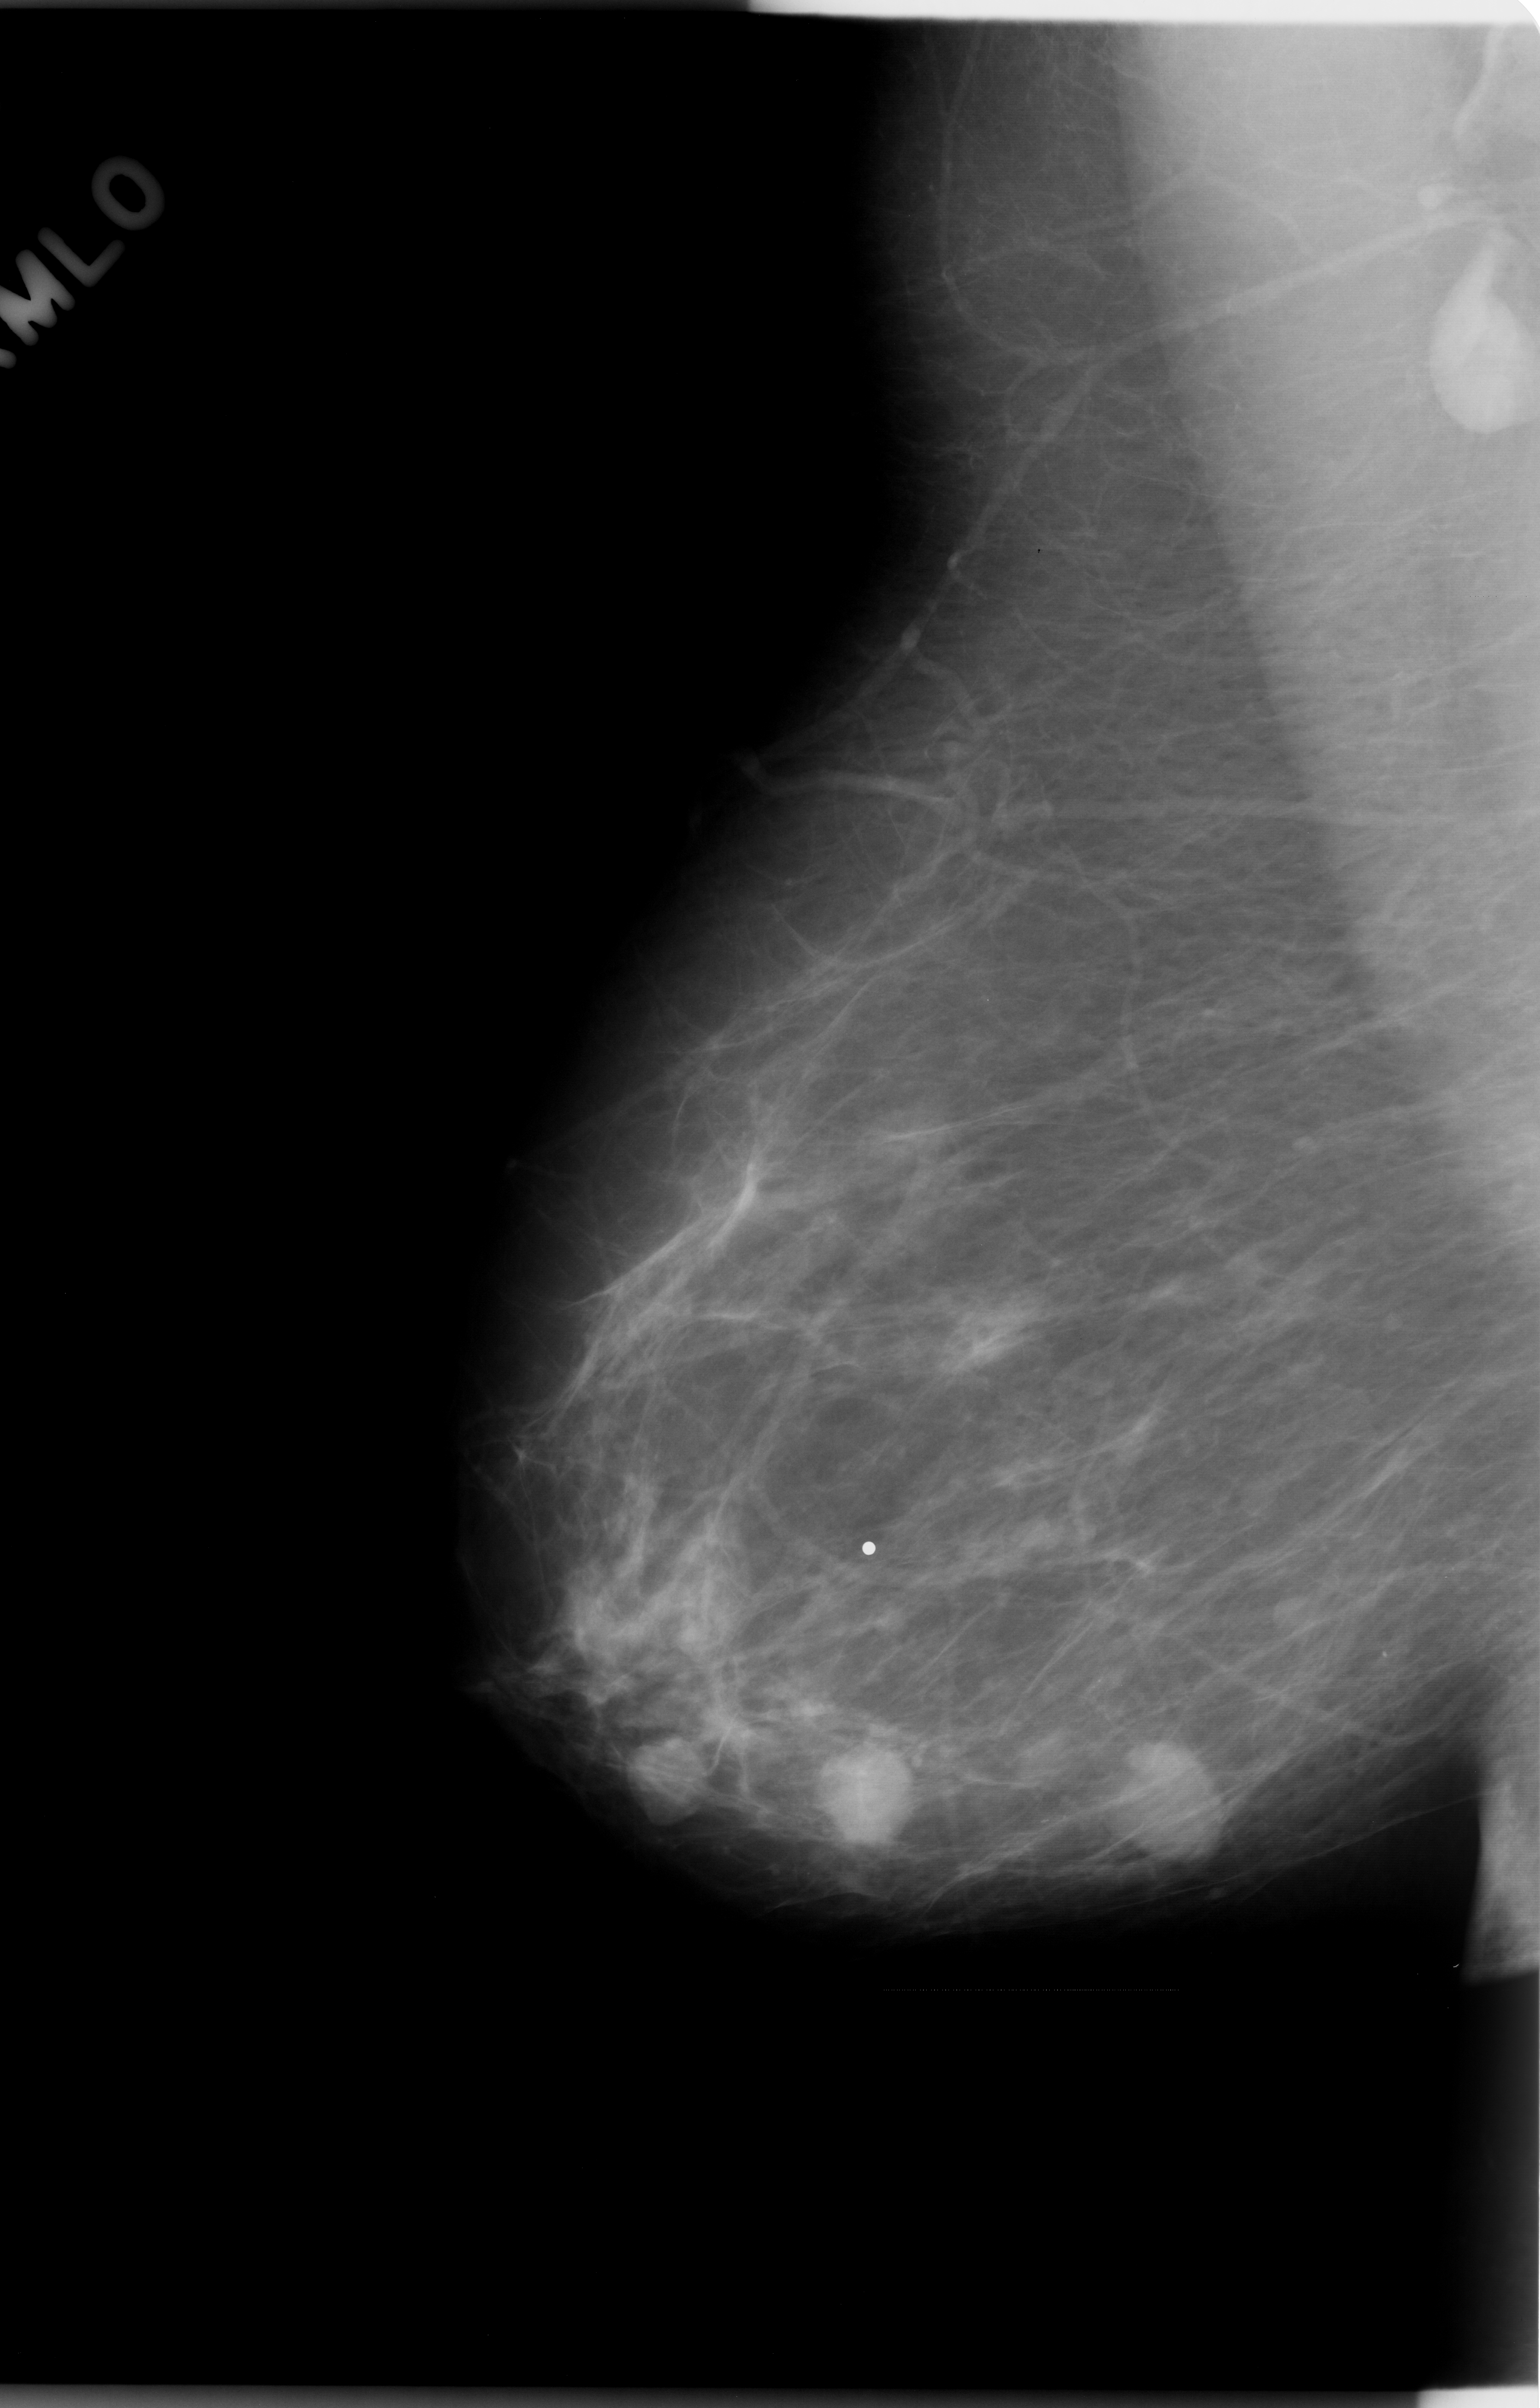
Digitized screen-film mammogram; right breast; MLO view; breast composition: almost entirely fatty (BI-RADS density category 1 of 4); 1540 × 2408 image matrix.
Expert-marked regions of interest on this image (one box per marked abnormality):
- Finding 1 of 3: mass, shape oval, margins circumscribed; BI-RADS assessment category 4; subtlety rating 5 on a 1 (subtle) to 5 (obvious) scale; pathology result (as recorded, not read from the image): benign: box from (x=606, y=1698) to (x=729, y=1820) px
- Finding 2 of 3: mass, shape oval, margins microlobulated; BI-RADS assessment category 4; pathology result (as recorded, not read from the image): malignant: (x=811, y=1730)–(x=928, y=1859)
- Finding 3 of 3: mass, shape oval, margins microlobulated; BI-RADS assessment category 4; subtlety rating 5 on a 1 (subtle) to 5 (obvious) scale; pathology (as recorded): malignant: (x=1074, y=1733)–(x=1205, y=1862)